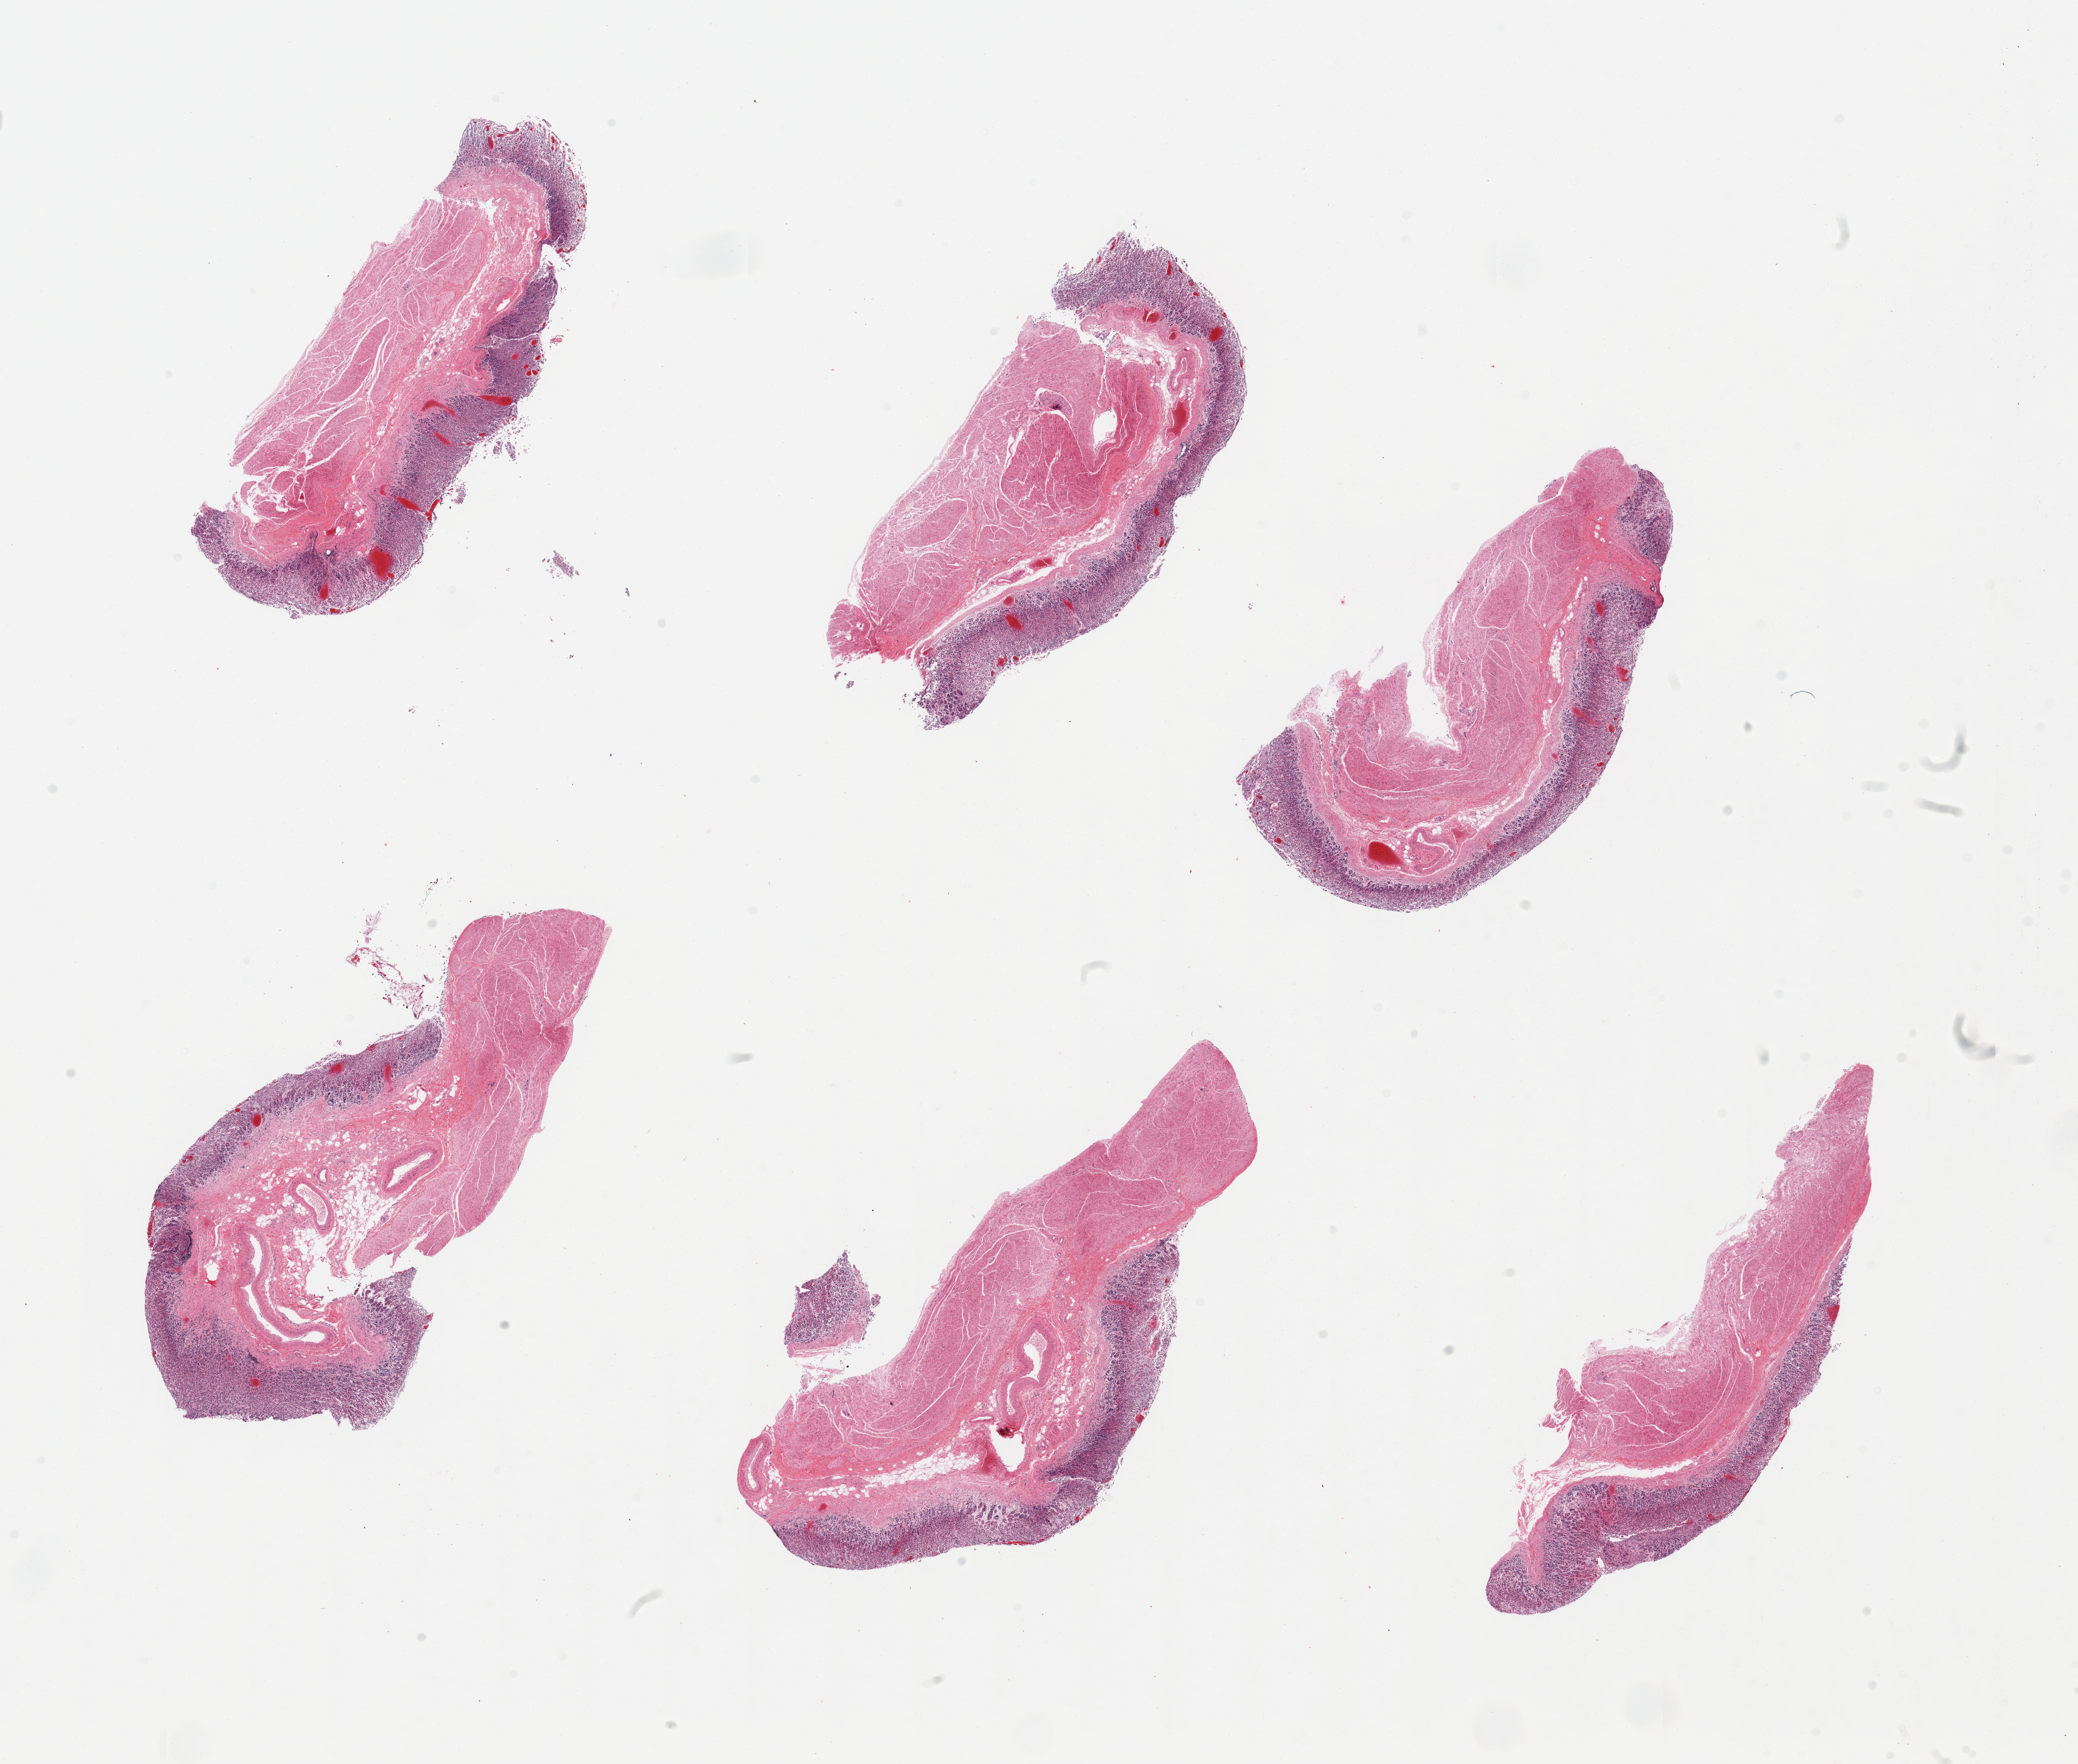
Whole-slide image, haematoxylin and eosin stain, brightfield, a low-resolution overview of the entire scanned area, about 24.6 x 20.9 mm (acquisition: 20x scan), PAXgene-fixed paraffin-embedded (PFPE) section, section of stomach (target tissue), tissue donor sample. Donor sex: male.
- review note (as recorded): 6 pieces mucosa up to ~20% thickness, but with advanced autolysis